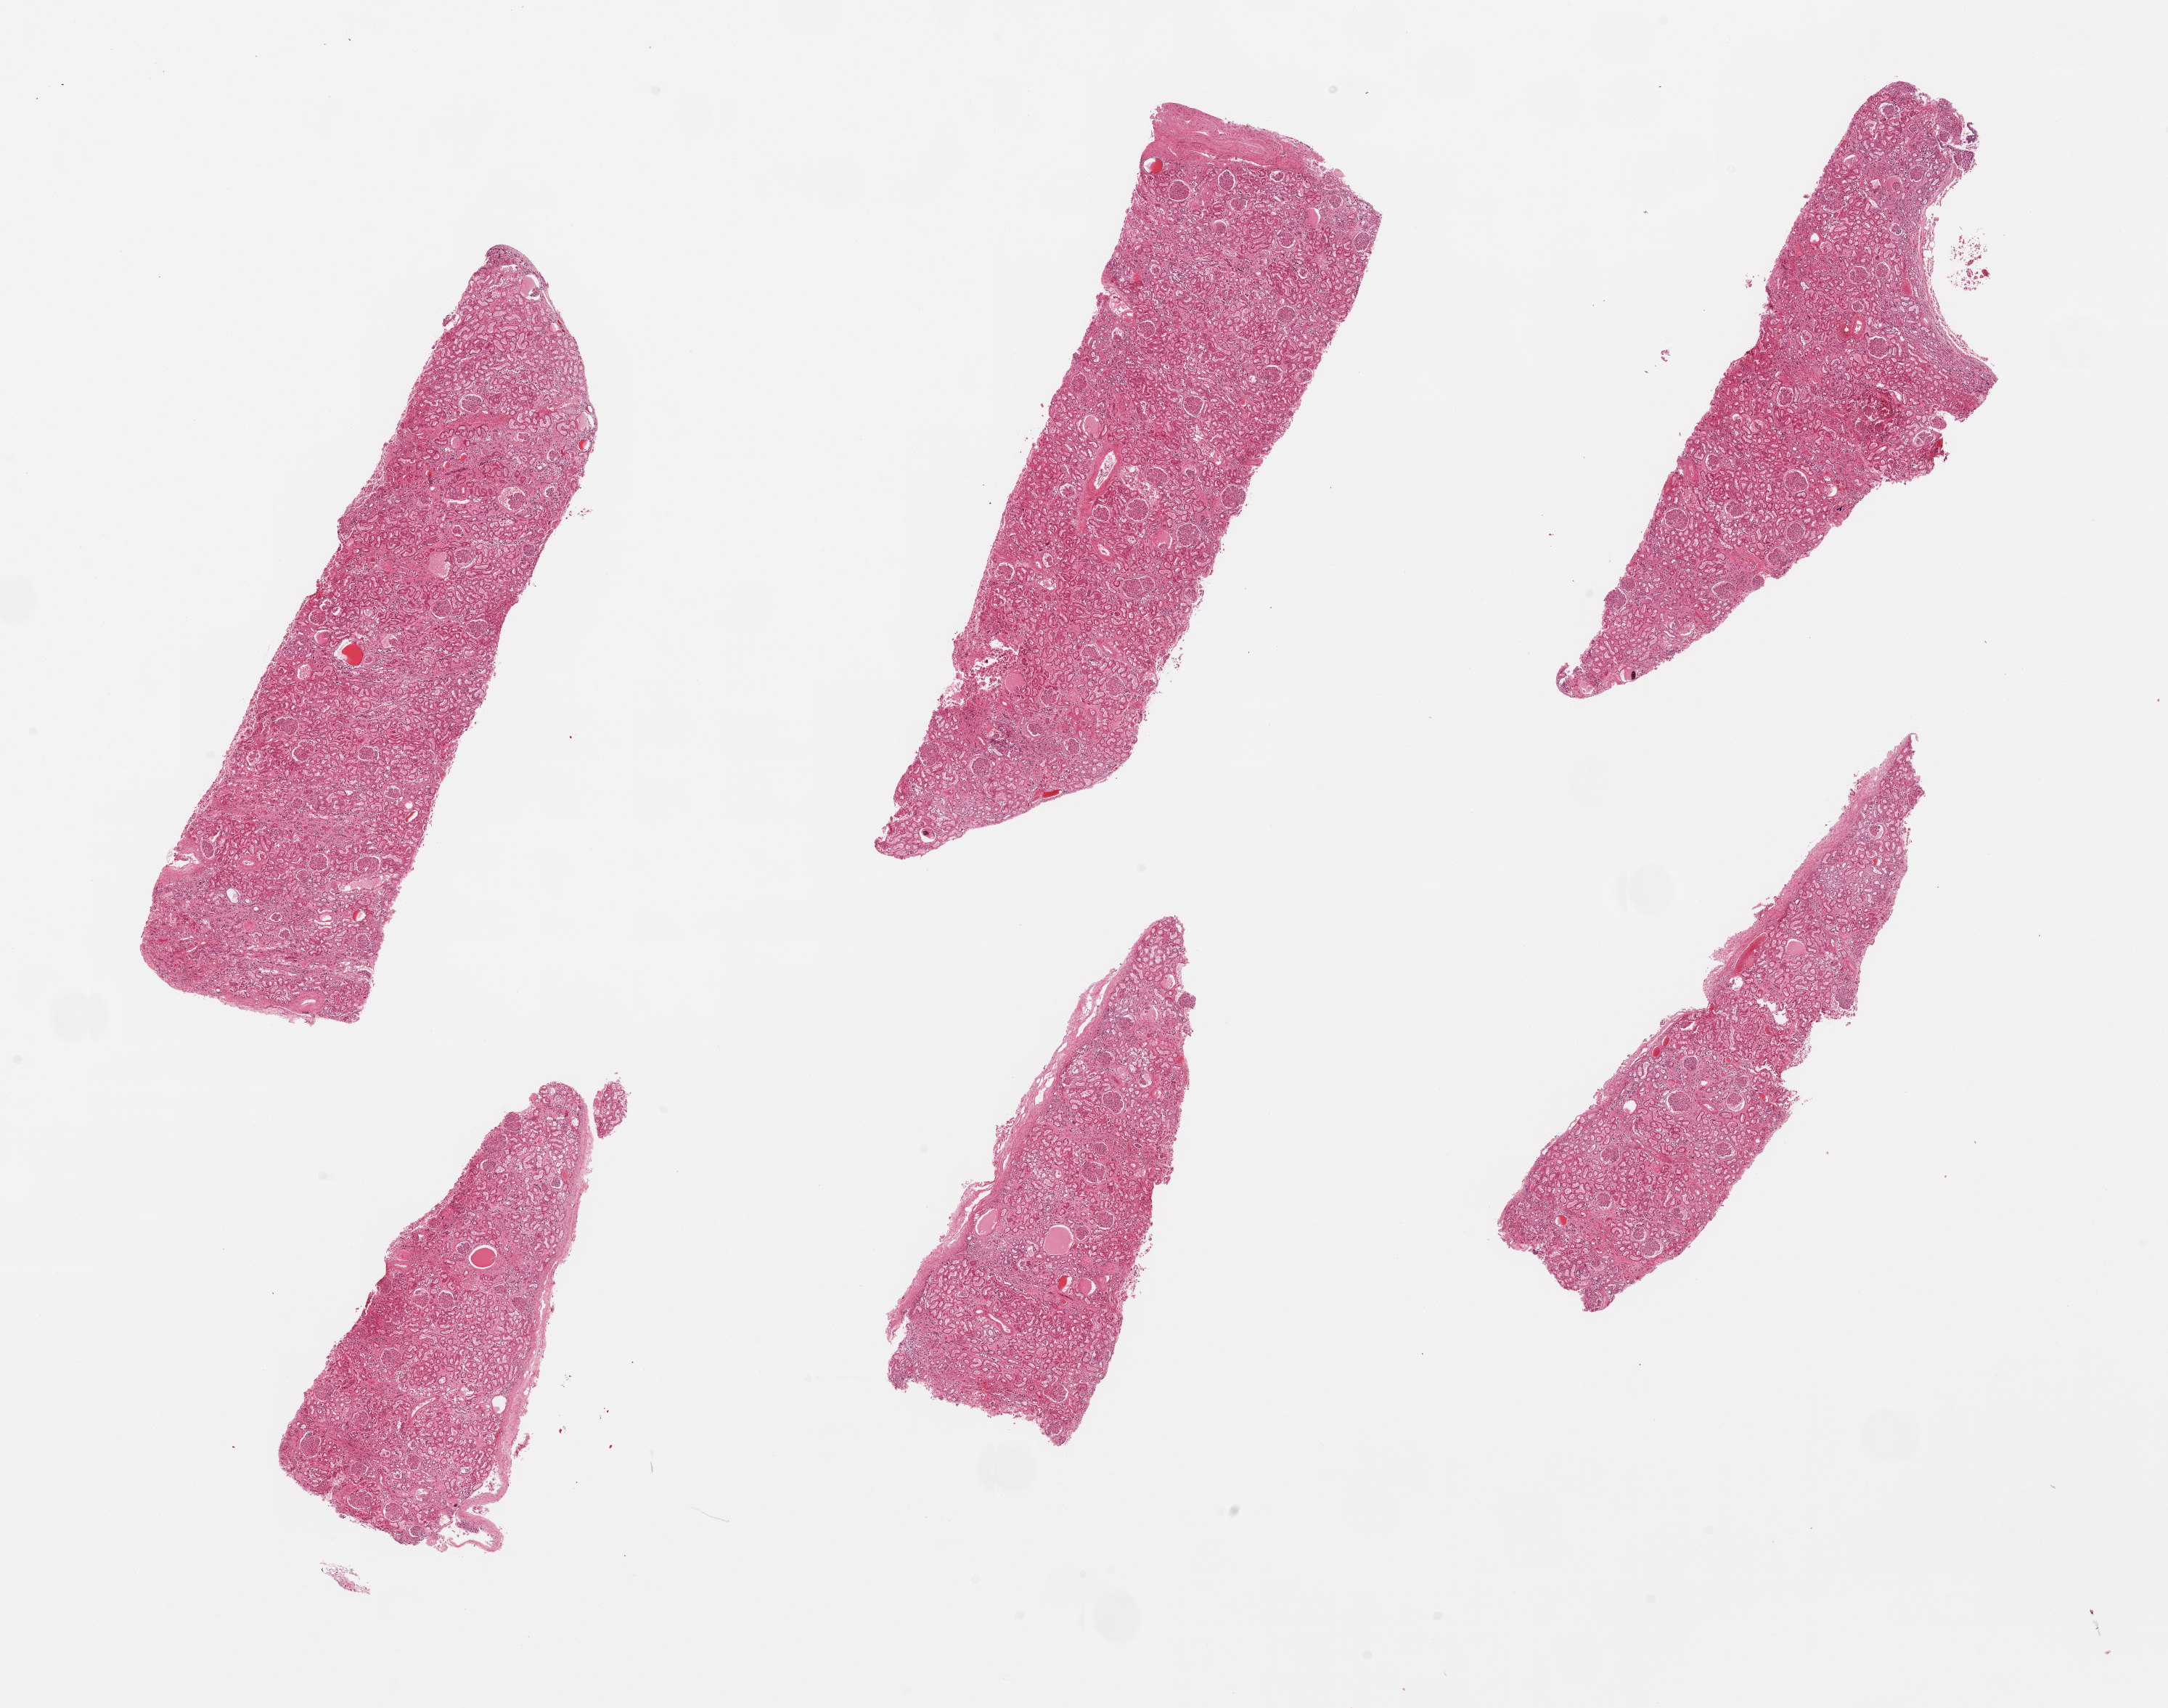
Digitized haematoxylin and eosin-stained section — a low-resolution overview of the entire scanned area, about 23.6 x 18.6 mm. PAXgene-fixed, paraffin-embedded tissue. Section of renal cortex (target tissue). Tissue donor sample. Donor: male.
Review note (as recorded): 6 pieces, glomeruli present; mild interstitial hyalinization.